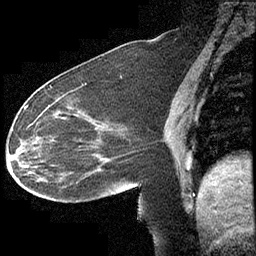
Breast MRI (dynamic contrast-enhanced), one sagittal slice; slice 162 of 232 in the series (ordered by position); dynamic contrast-enhanced study with each time point stored as its own series, time point 2 of 4 at this slice position (early post-contrast, ordered by acquisition time); 1.5 T; TE 4.2 ms, TR 6.7 ms; 3 mm slice thickness; 256 × 256 image matrix. Female patient, age 63 years. Case-level facts recorded for this patient, not image findings: setting: breast cancer imaged before/during neoadjuvant chemotherapy; receptor status: triple-negative.
Outlined on this slice (semi-automatically segmented with operator editing):
- analysis volume of interest (the breast-tissue region the enhancement analysis was run in; not a lesion): box from (x=13, y=90) to (x=140, y=211) px
- tumour enhancement mask (voxels above the 70 % enhancement threshold inside the analysis volume of interest): (x=24, y=91)–(x=94, y=155)